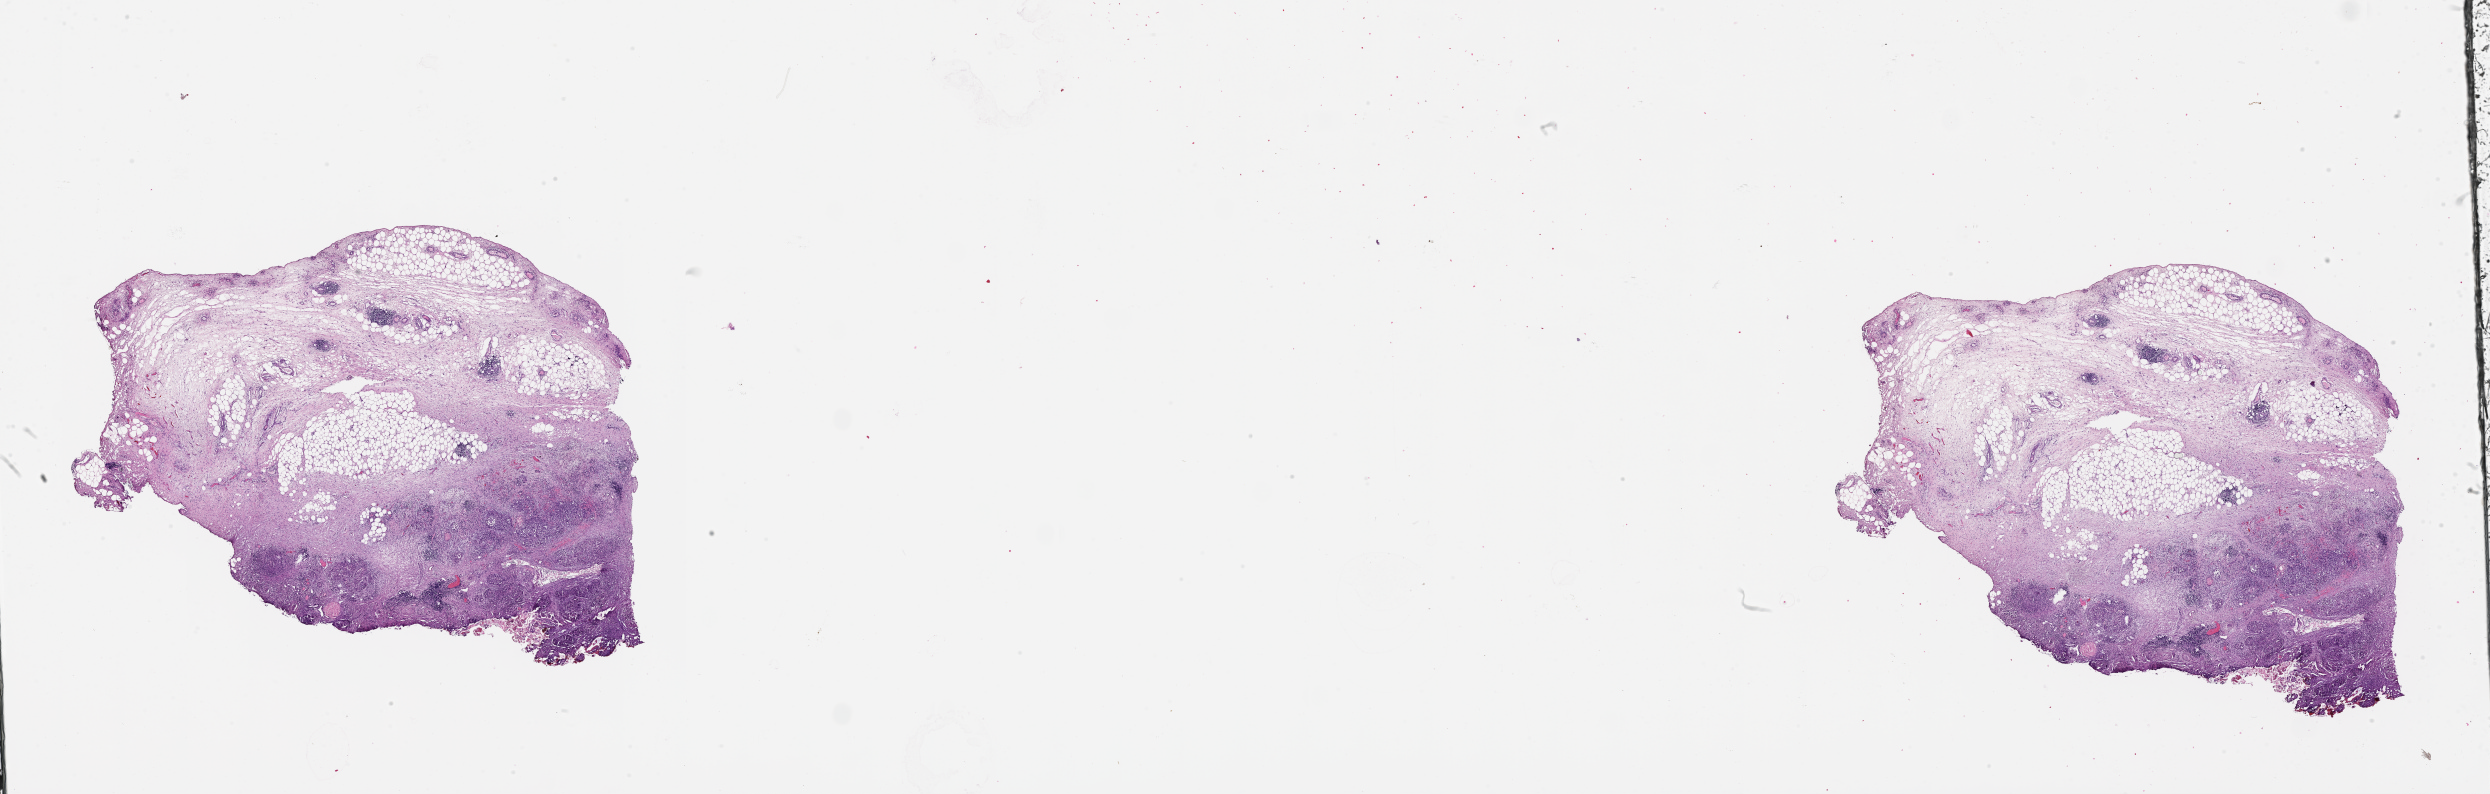
H&E-stained whole-slide image, low-resolution overview of the scanned area, about 40.1 x 12.8 mm. Pancreas, normal (non-tumour) tissue. 69-year-old male patient.
This section: normal (non-tumour) tissue from the same patient. Patient diagnosis: Infiltrating duct carcinoma, NOS.